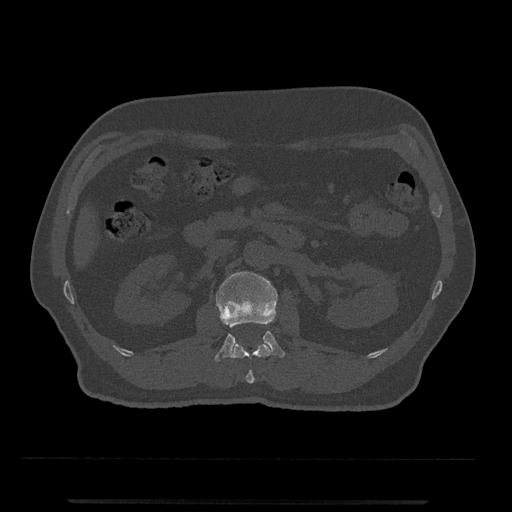
CT including the spine, one axial slice; slice 295 of 797 in the series (ordered by position); 120 kVp; bone window (W 1800 / L 400 HU); 512 × 512 image matrix. Patient: male, 63 years. From the clinical record (not read from this slice): primary cancer: prostate.
Outlined on this slice (semi-automatic segmentation, software-assisted and operator-edited):
- L1 vertebra: bounding box (x1, y1, x2, y2) in pixels: (231, 342, 273, 384)
- L2 vertebra: (214, 271, 285, 362)